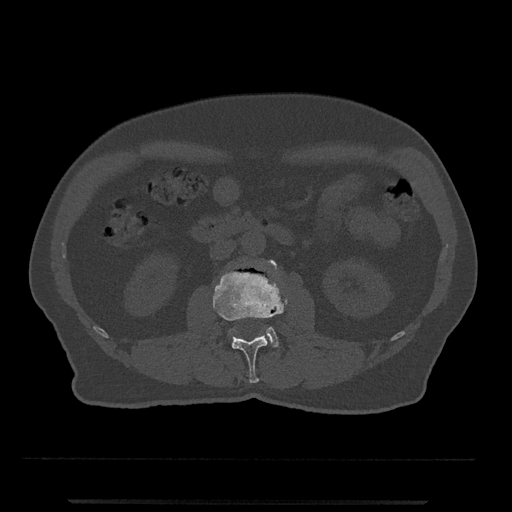
CT including the spine, one axial slice; position 247 of 797 along the scan axis; bone window (W 1800 / L 400 HU); 512 × 512 image matrix, field of view 419 × 419 mm. Patient: male, 63 years. From the clinical record (not read from this slice): primary cancer: prostate.
Annotated regions visible in this slice (semi-automatic segmentation, software-assisted and operator-edited):
- L2 vertebra: bounding box [x1, y1, x2, y2] px = [213, 261, 288, 383]
- L3 vertebra: [266, 260, 278, 347]